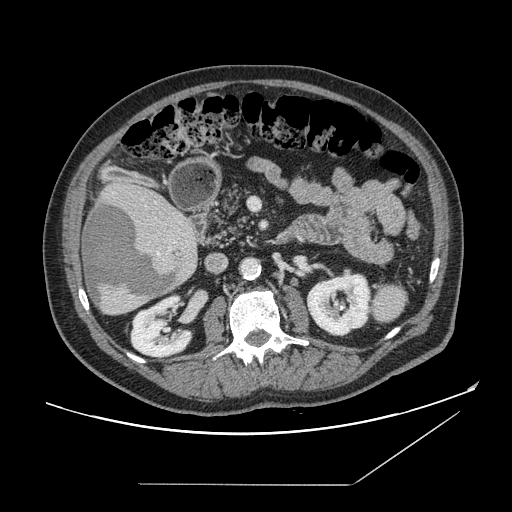
Contrast-enhanced abdominal CT, one axial slice; slice 66 of 166 in the series (ordered by position); intravenous contrast given; soft-tissue window (W 400 / L 40 HU); 512 × 512 image matrix. Male patient, age 80 years. Case-level facts recorded for this patient, not image findings: diagnosis: colorectal cancer liver metastases, imaged before liver resection; multiple liver metastases: no; largest metastasis: 2.2 cm; chemotherapy before resection: no.
Annotated regions visible in this slice (expert manual segmentation):
- liver: bounding box (x1, y1, x2, y2) in pixels: (81, 183, 199, 316)
- planned liver remnant (the part of the liver to remain after resection): (116, 183, 177, 212)
- liver metastasis: (84, 202, 180, 307)